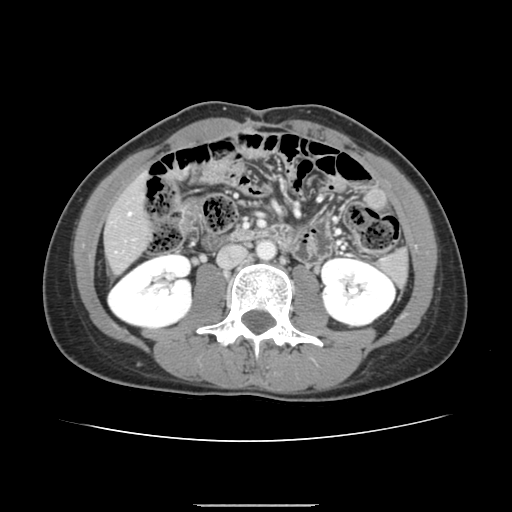
Contrast-enhanced abdominal CT, one axial slice; slice 45 of 150 in the series (ordered by position); soft-tissue window (W 400 / L 40 HU); 2.5 mm slice thickness; 512 × 512 image matrix, field of view 324 × 324 mm. Female patient, age 32 years. From the clinical record (not read from this slice): diagnosis: colorectal cancer liver metastases, imaged before liver resection; multiple liver metastases: yes; largest metastasis: 0.7 cm; disease in both lobes: no.
Structures marked on this image (outlined manually by an expert reader):
- hepatic veins: bounding box (x1, y1, x2, y2) in pixels: (128, 212, 131, 215)
- liver: (106, 180, 150, 271)
- planned liver remnant (the part of the liver to remain after resection): (106, 181, 150, 271)